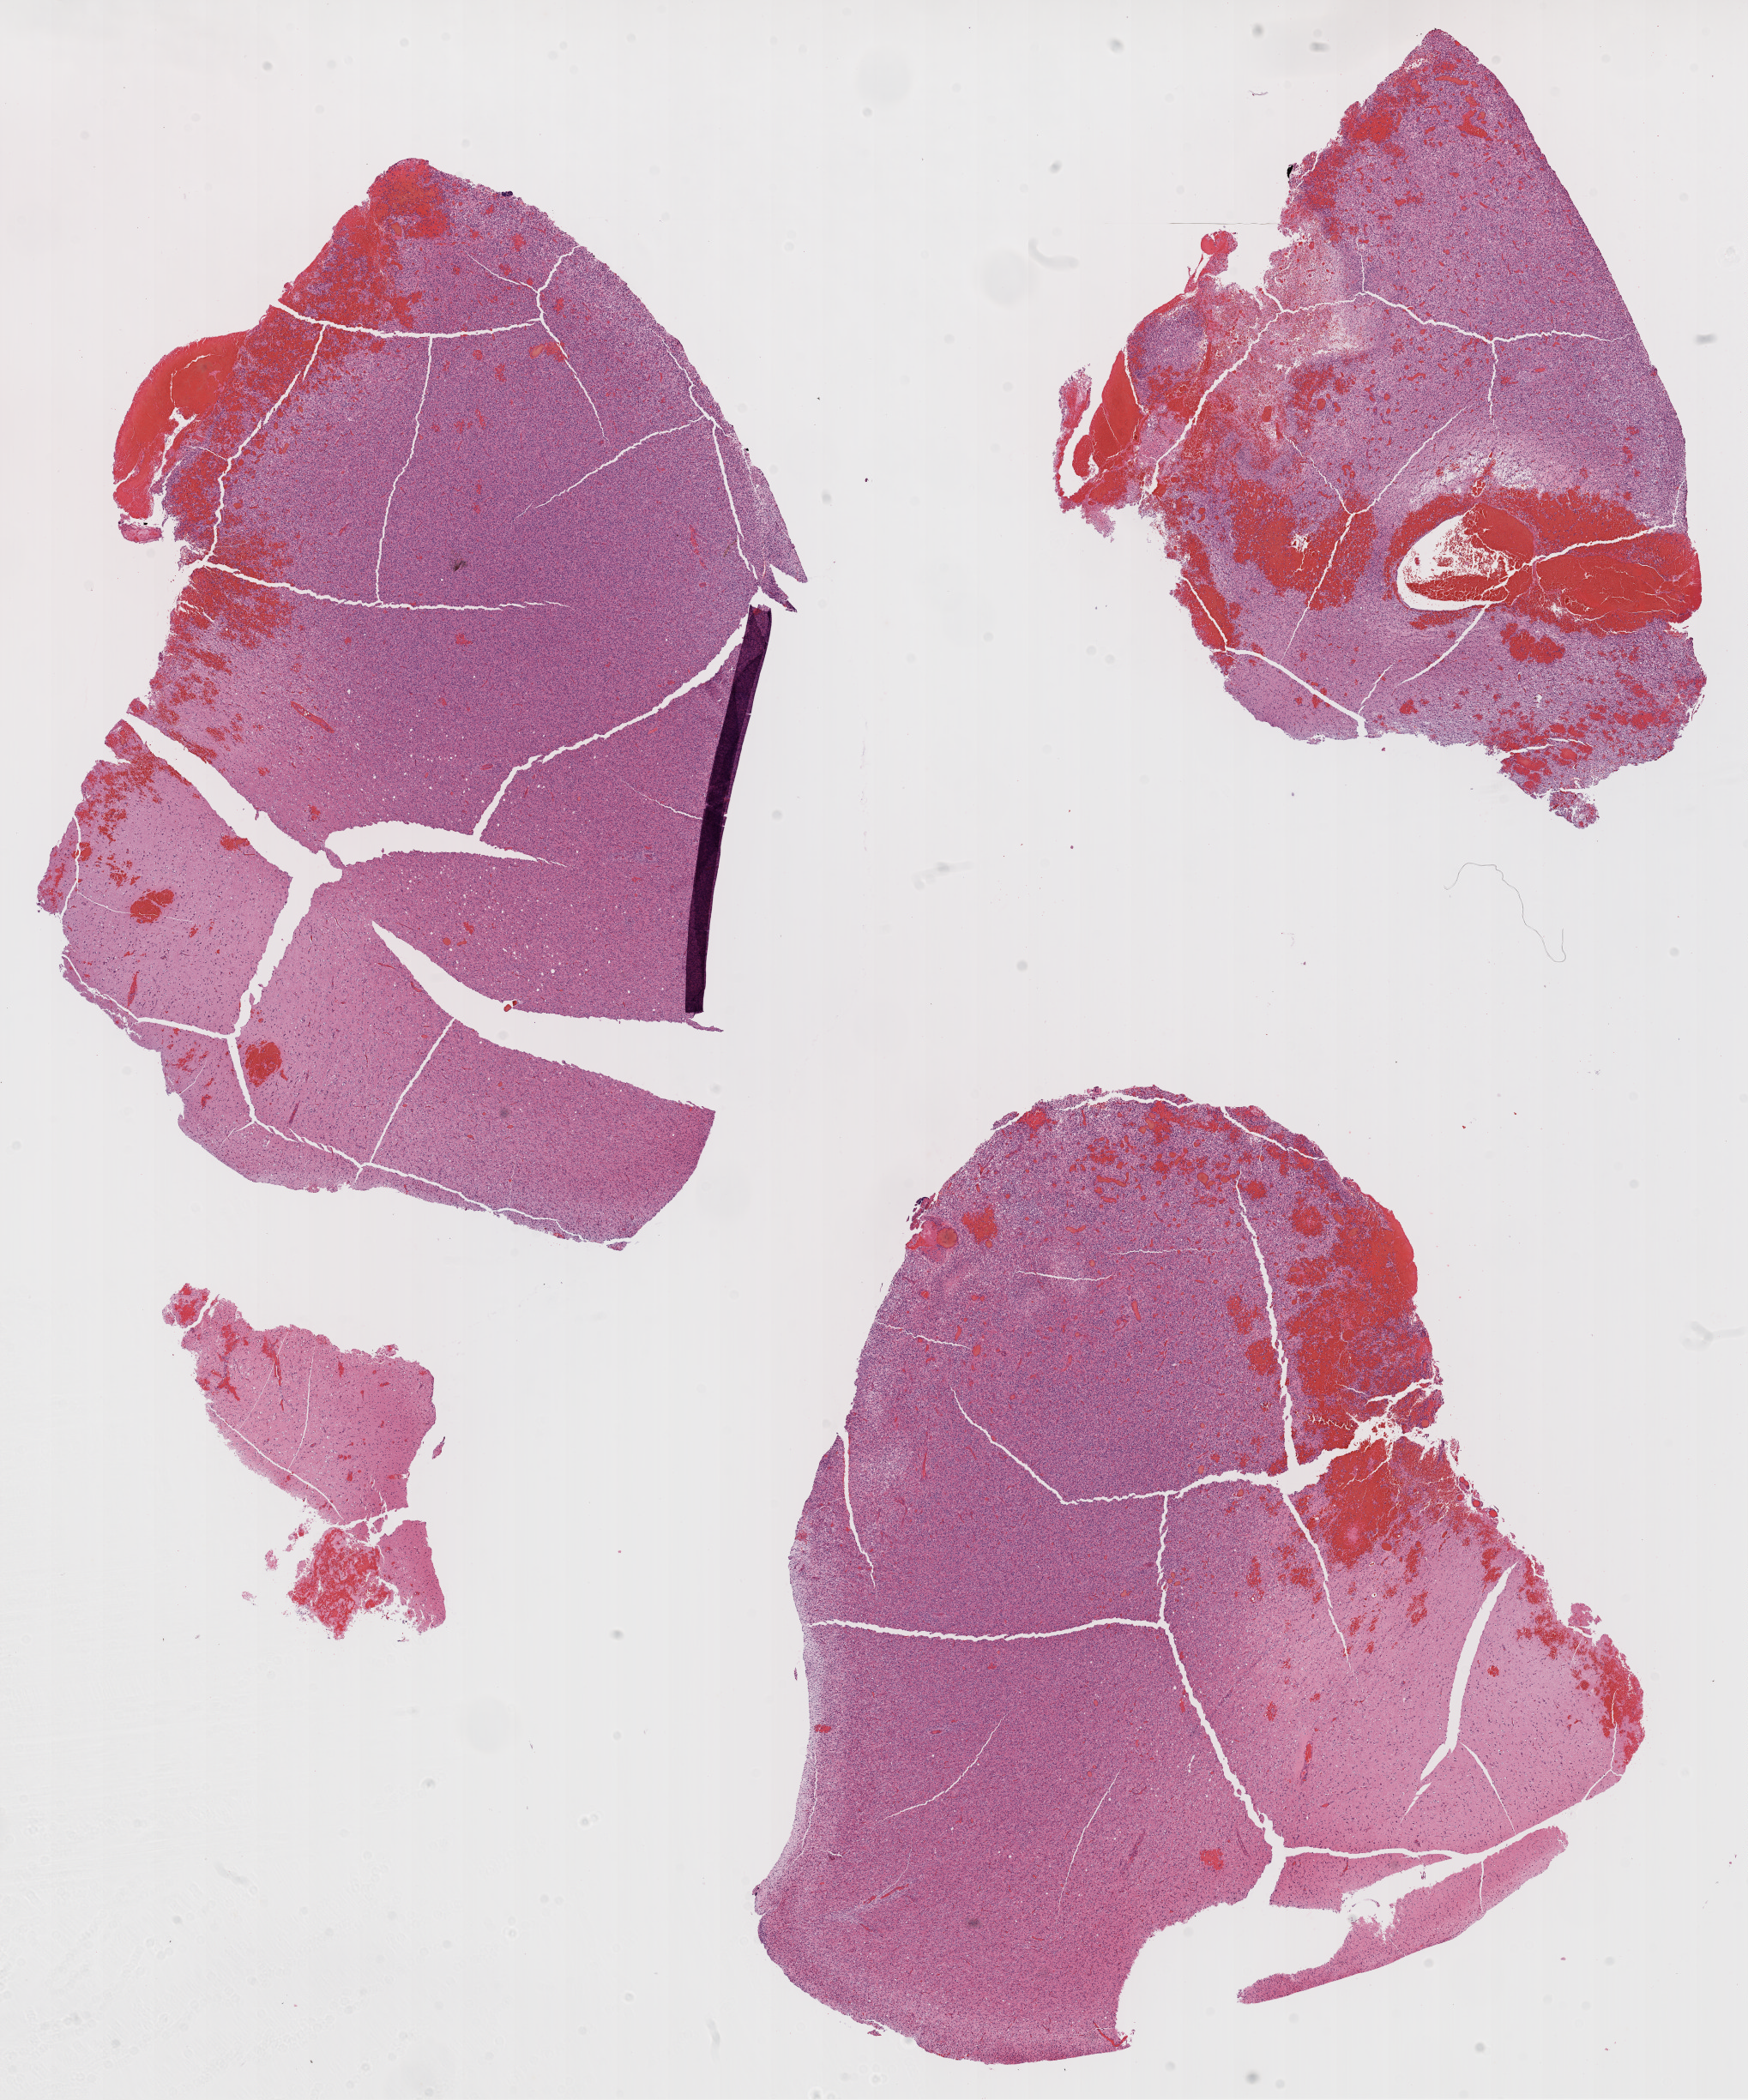
Hematoxylin and eosin (H&E) stained whole-slide image, shown as a low-resolution overview of the whole scanned area (about 16.4 x 19.8 mm, acquisition: 20x scan). Formalin-fixed paraffin-embedded (FFPE) diagnostic section. Sample: primary tumour, brain. Male, age 54 years at initial diagnosis.
• histologic diagnosis: Glioblastoma